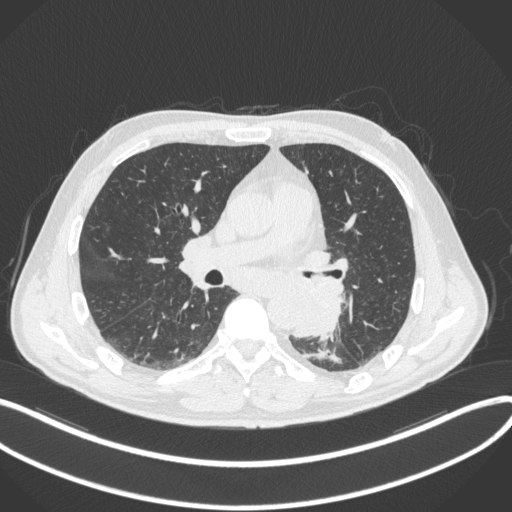
Chest CT, one axial slice. Position 183 of 328 along the scan axis. 120 kVp. Lung window (W 1500 / L -600 HU). 512 × 512 image matrix, field of view 400 × 400 mm. Patient: male, 59 years. Case-level facts recorded for this patient, not image findings: clinical TNM (as recorded): T2a N2 M0.
Outlined on this slice (bounding box drawn by a radiologist):
- lung tumour (recorded histology: squamous cell carcinoma): bounding box (x1, y1, x2, y2) in pixels: (290, 287, 345, 340)